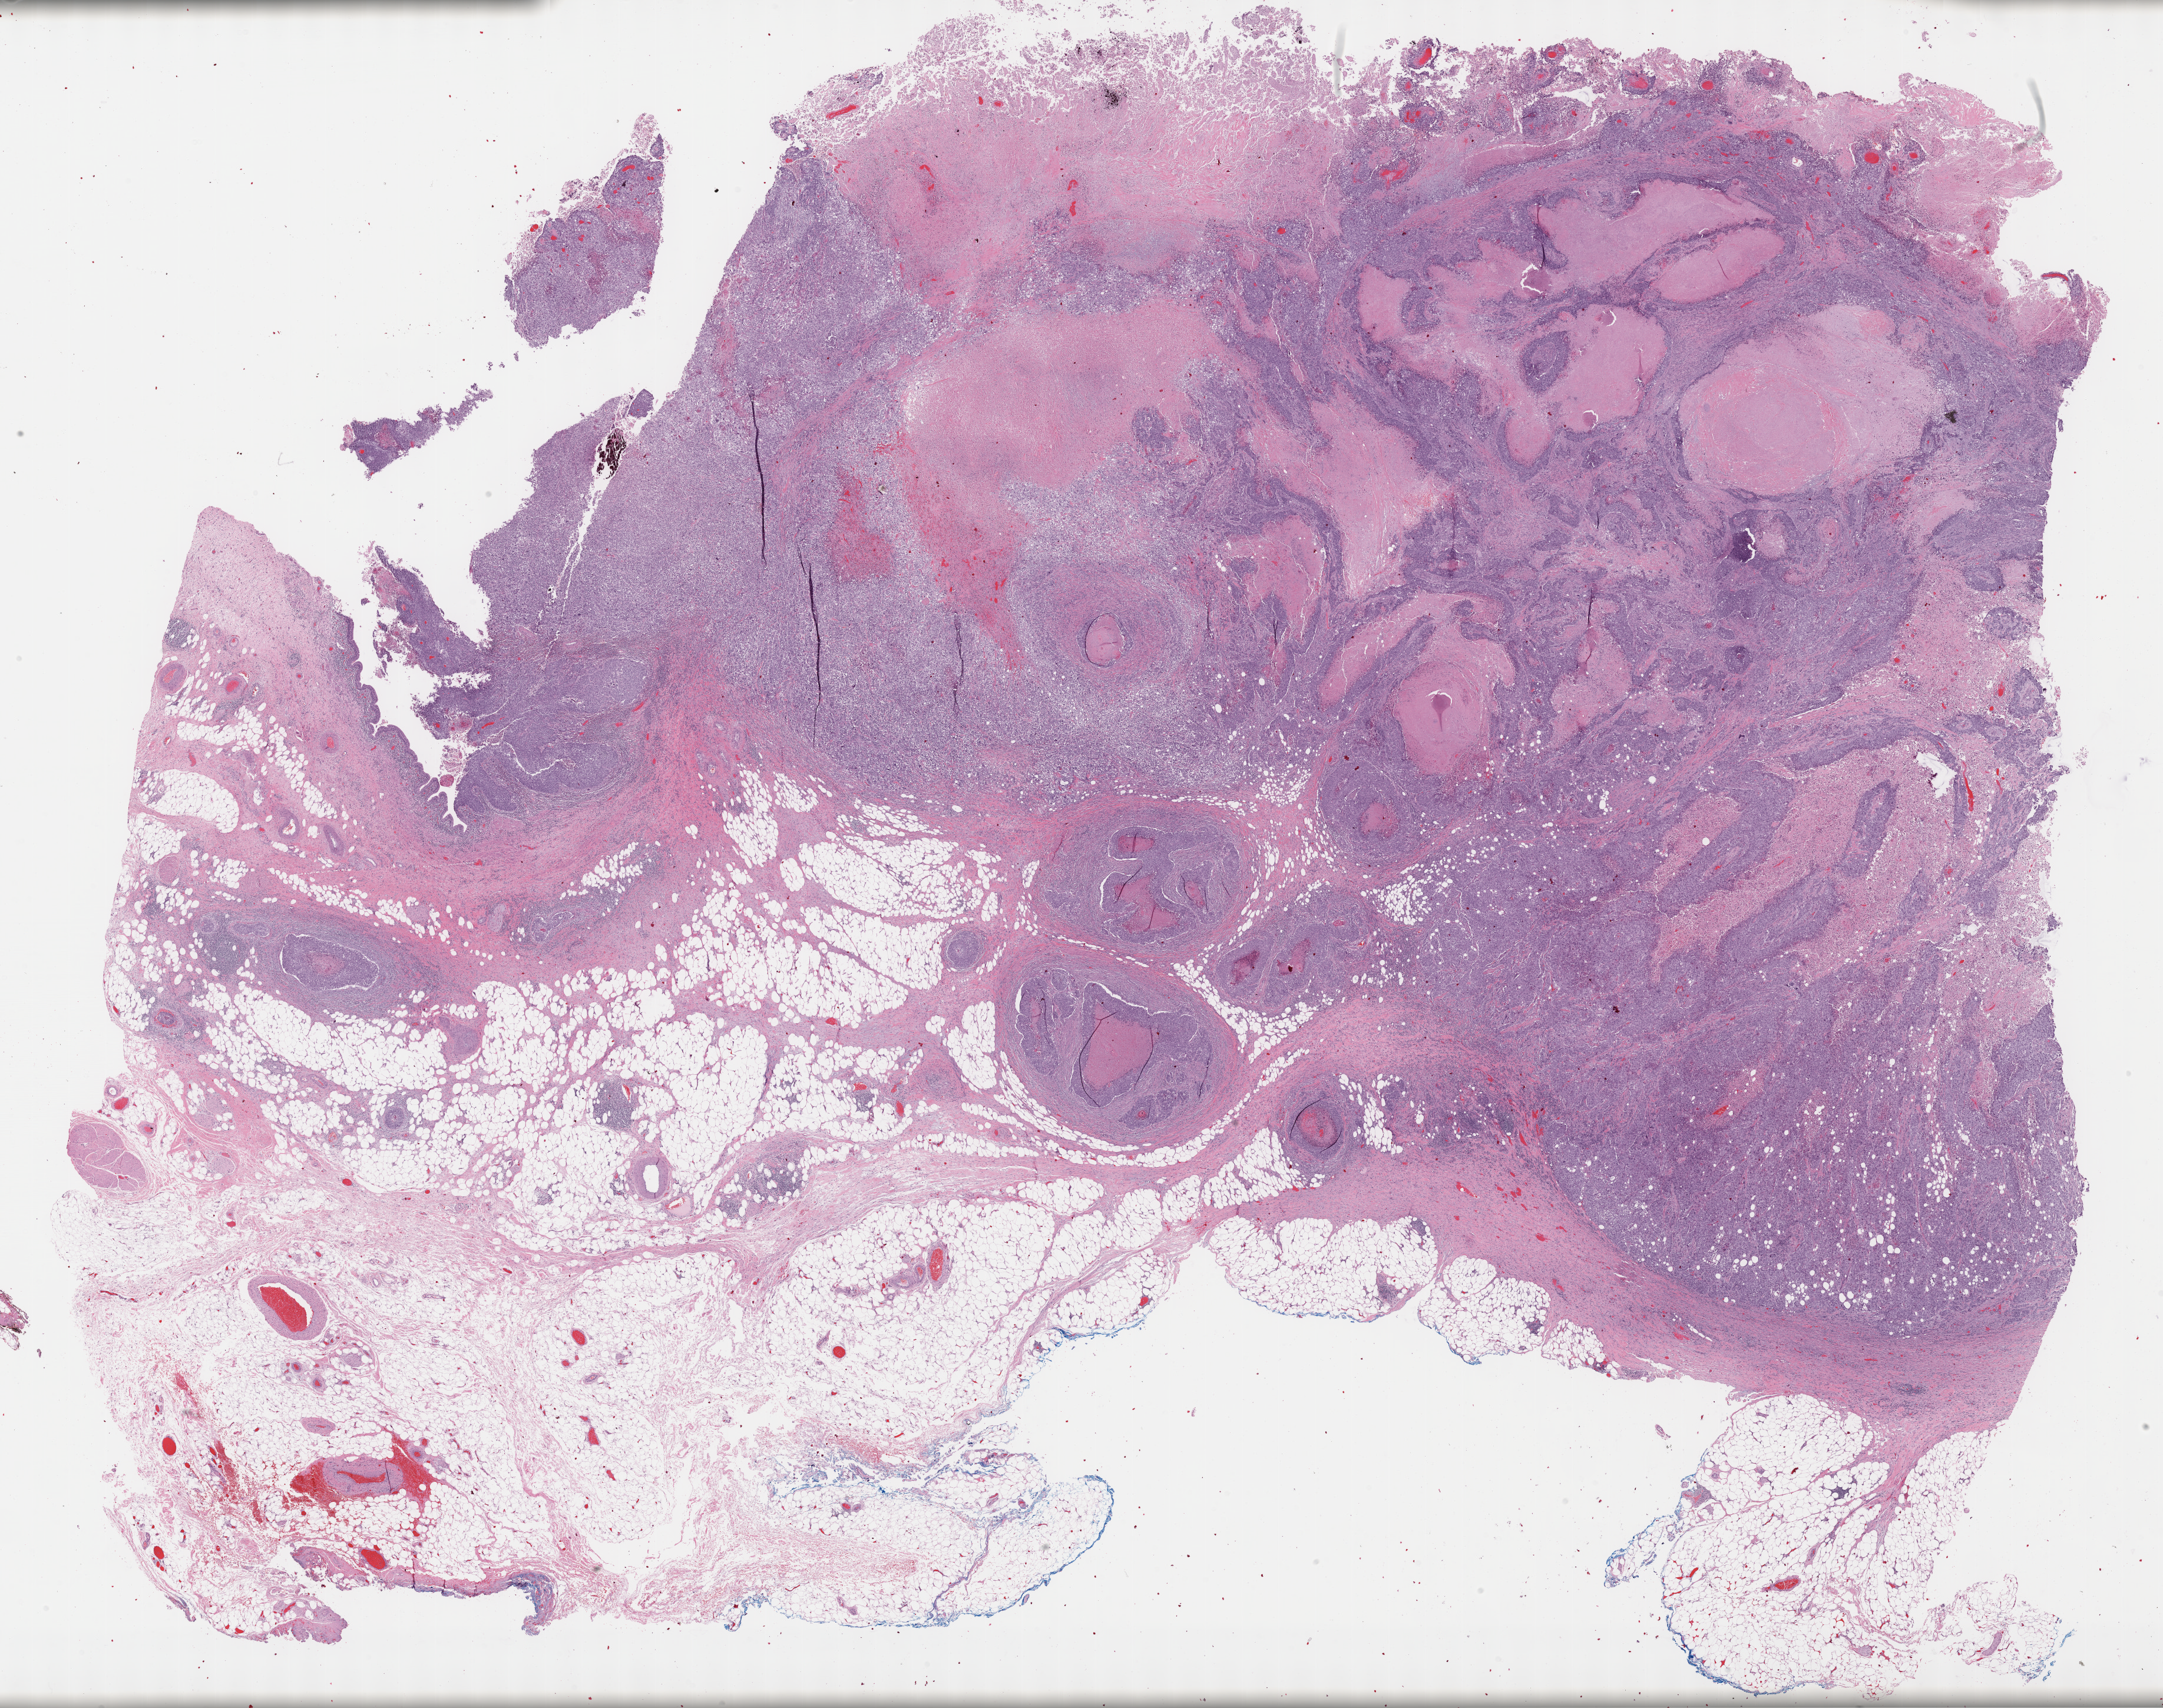
Digitized H&E-stained tissue section (whole slide), a low-resolution overview of the entire scanned area, about 29.7 x 23.5 mm (from a 40x scan). Formalin-fixed paraffin-embedded (FFPE) diagnostic section. Primary tumour sample from the bladder. Male patient; age at initial diagnosis 76 years. Histologic grade: high grade.
Histologic diagnosis: Transitional cell carcinoma. AJCC pathologic stage: III (6th edition). Lymph nodes positive (case pathology): 0 of 8 examined.